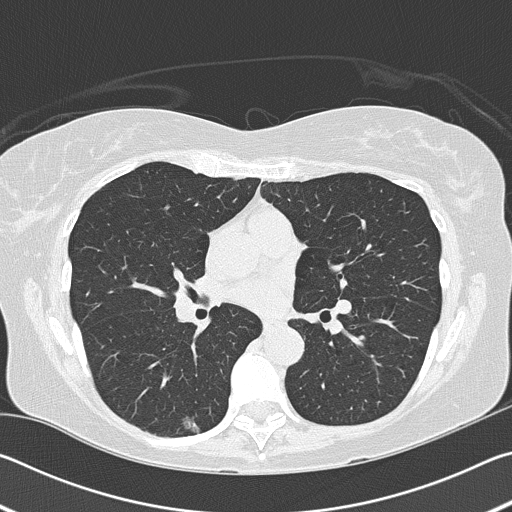
Low-dose screening chest CT, axial slice, baseline annual screen, lung window (W 1500 / L -600 HU), lung (sharp) reconstruction kernel (B50f), slice 76 of 159 in the series, 512 × 512 image matrix, field of view 340 × 340 mm. Female, age 60 years at enrolment. Former smoker at enrolment.
• Expert reader's lesion annotation, box from (x=171, y=407) to (x=215, y=442) px.
• The screening reader recorded 2 non-calcified nodules or masses ≥4 mm on this exam (right lower lobe, right middle lobe); which of them this box marks is not recorded.
• Lung cancer was diagnosed 799 days after this screen (after the third annual screen): acinar cell carcinoma, right lower lobe, moderately differentiated (G2), stage IA (AJCC 6th edition), 10 mm at pathology.